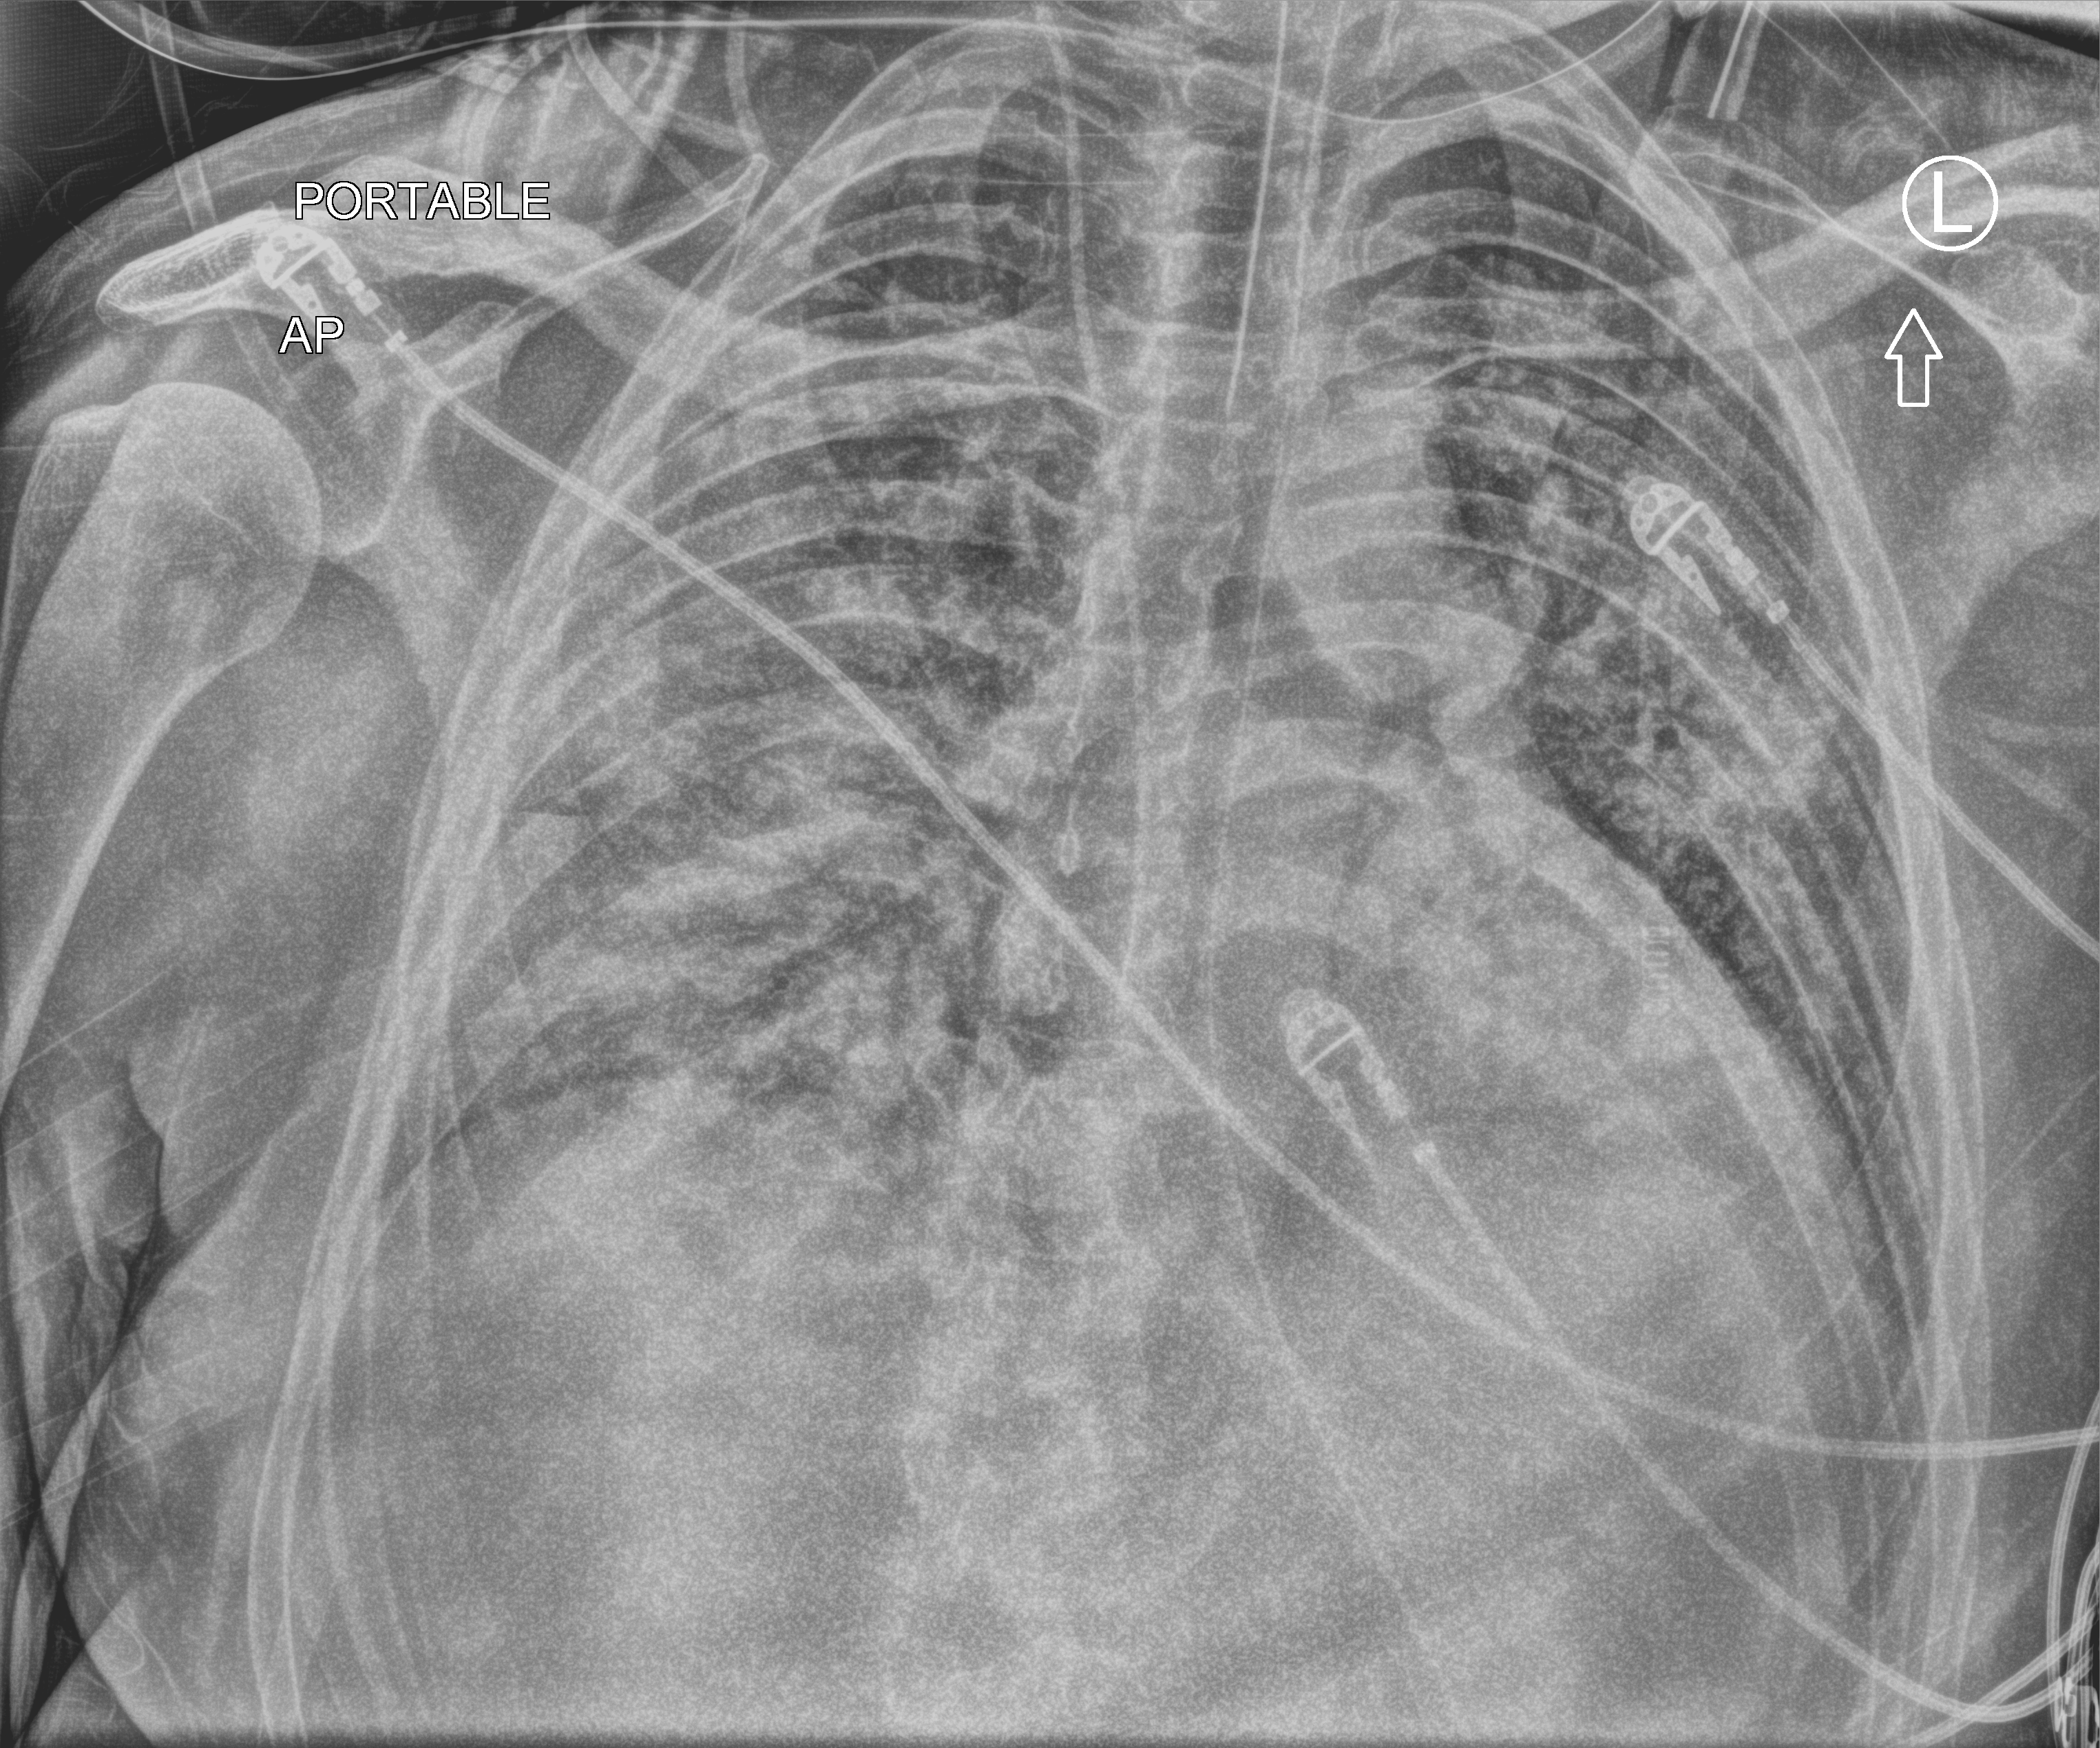
Portable chest radiograph; anteroposterior (AP) projection. Male patient hospitalised with COVID-19, age 18–59 years.
Hospital-stay facts (about this admission, not read from this image; timing relative to this image not recorded):
- mechanically ventilated during this hospital stay: yes
- diabetes (admission record): no